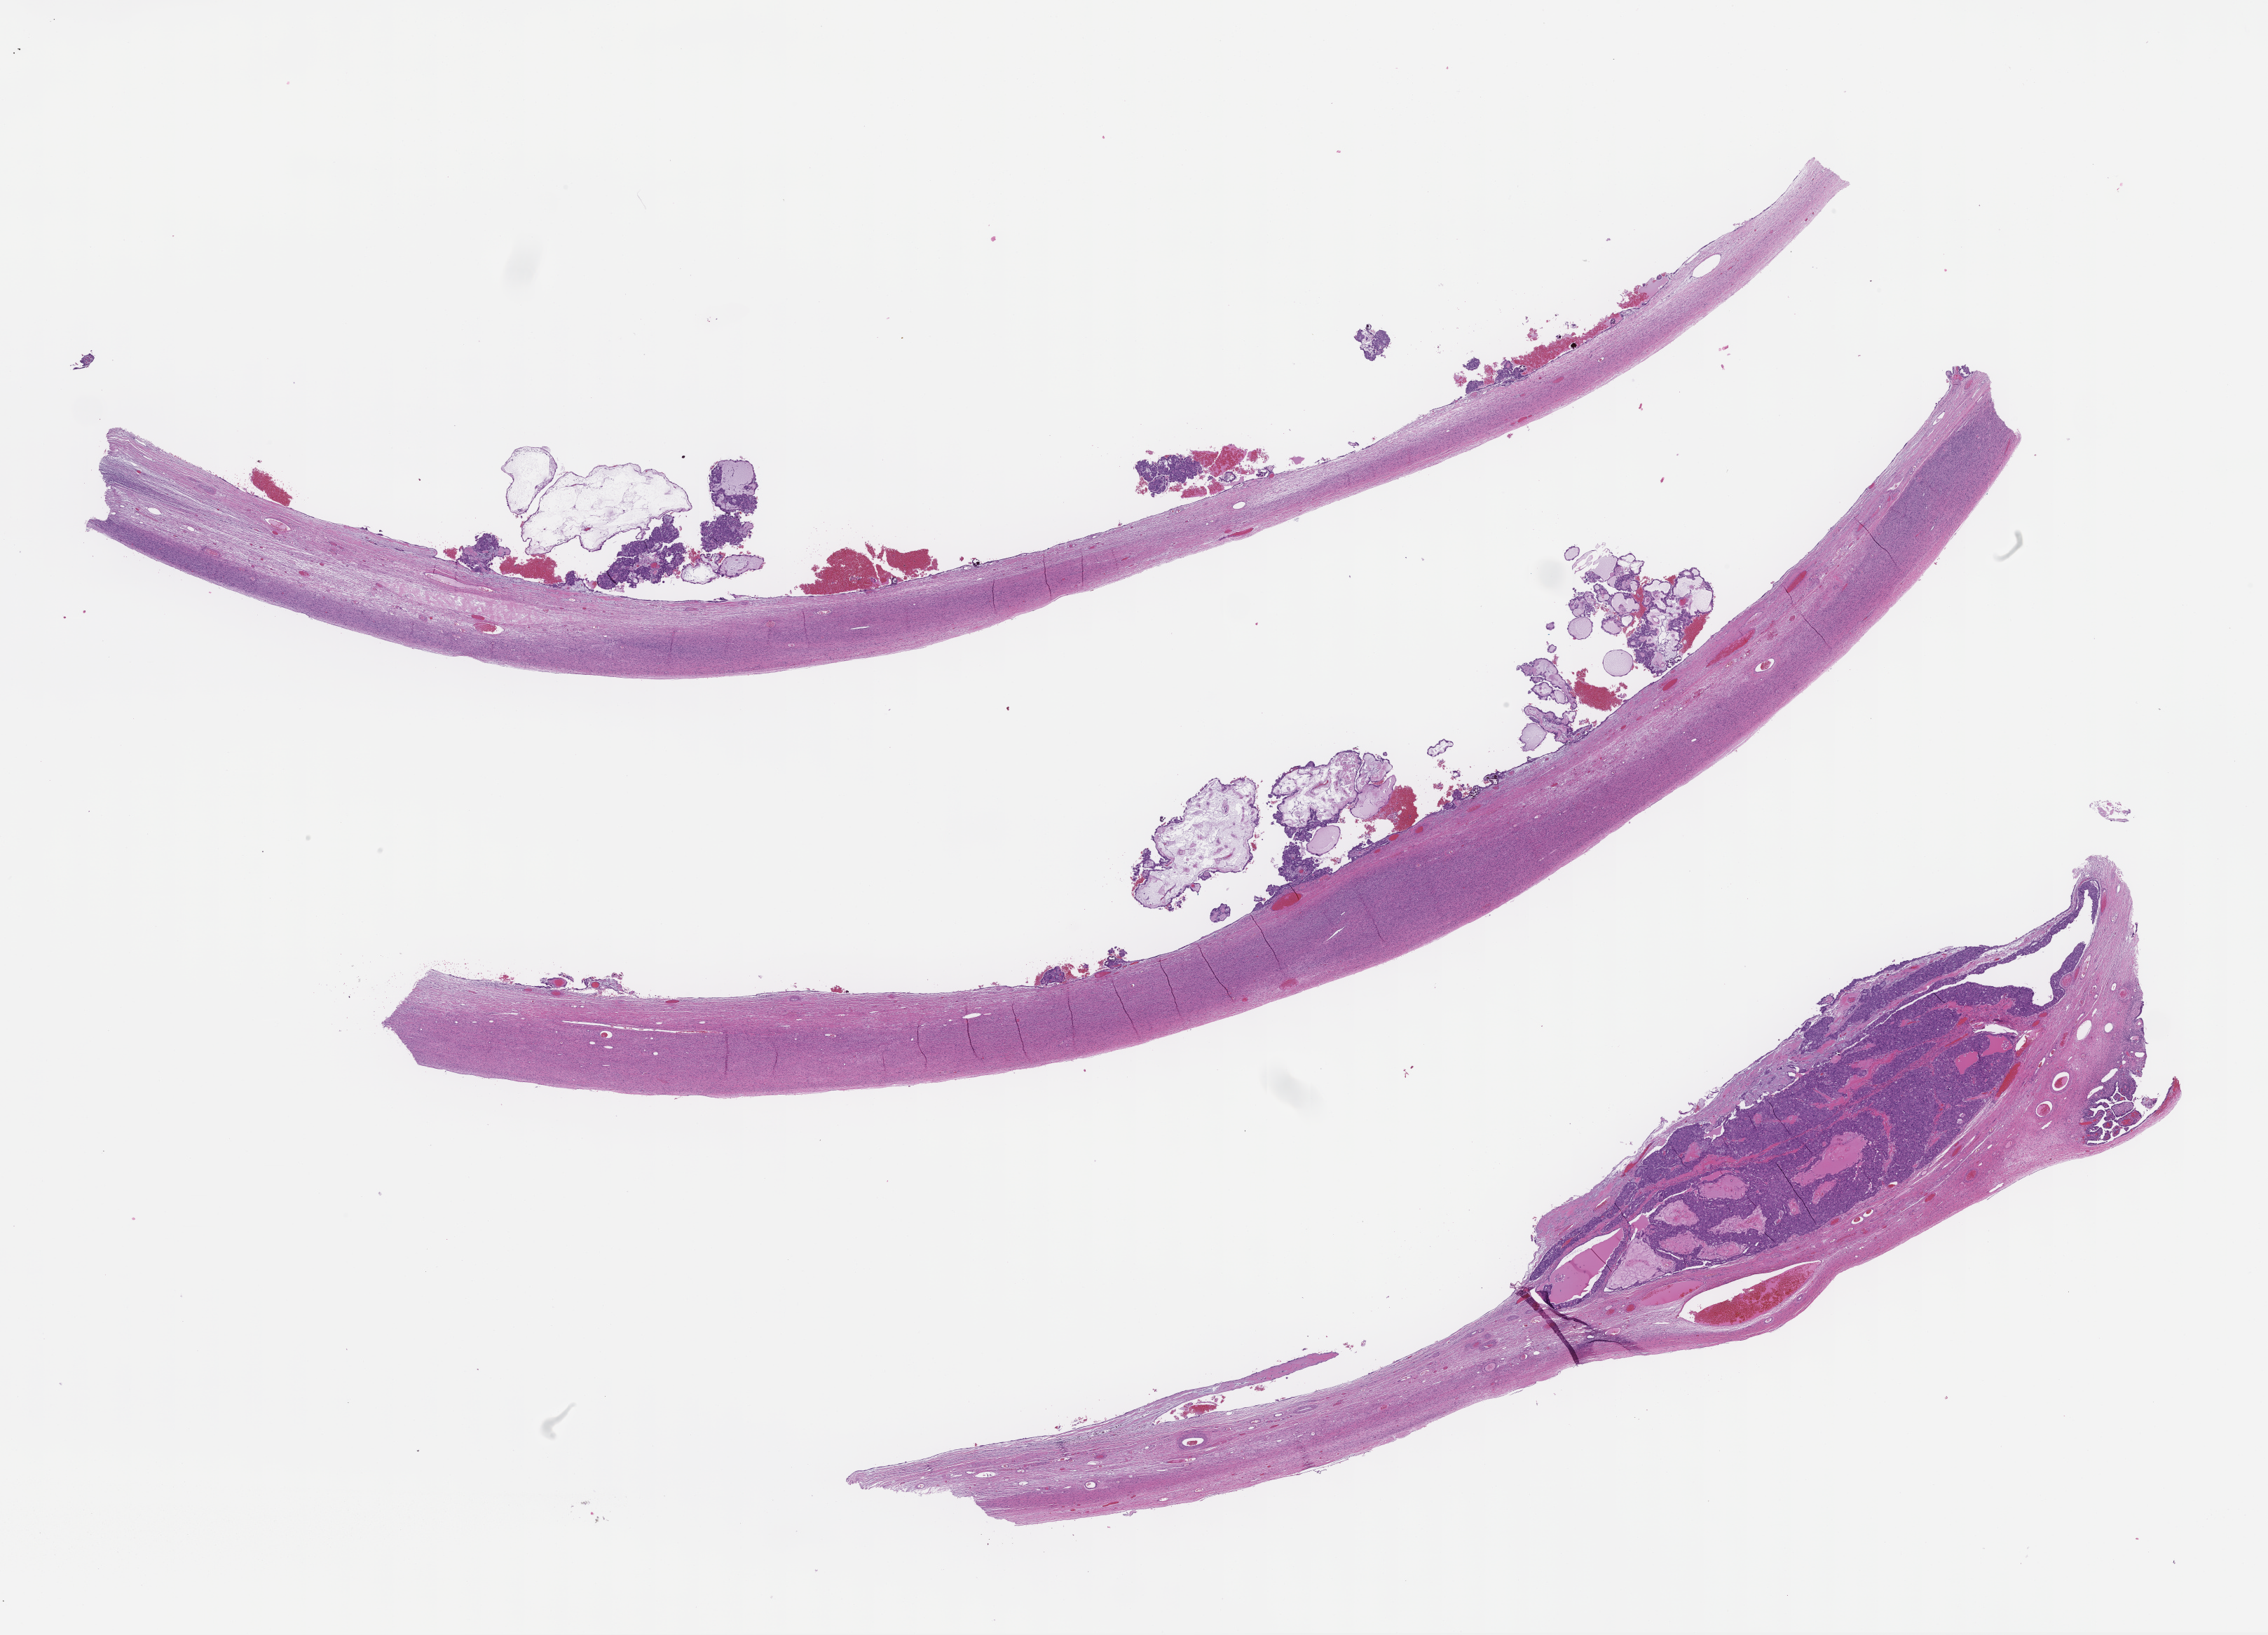
Hematoxylin and eosin (H&E) whole-slide image — low-resolution overview of the scanned area, about 26.1 x 18.8 mm. Formalin-fixed paraffin-embedded section. Site: ovary. Specimen time point: archival tissue. Female patient.
This section: primary tumor. Diagnosis: Ovarian Carcinoma.